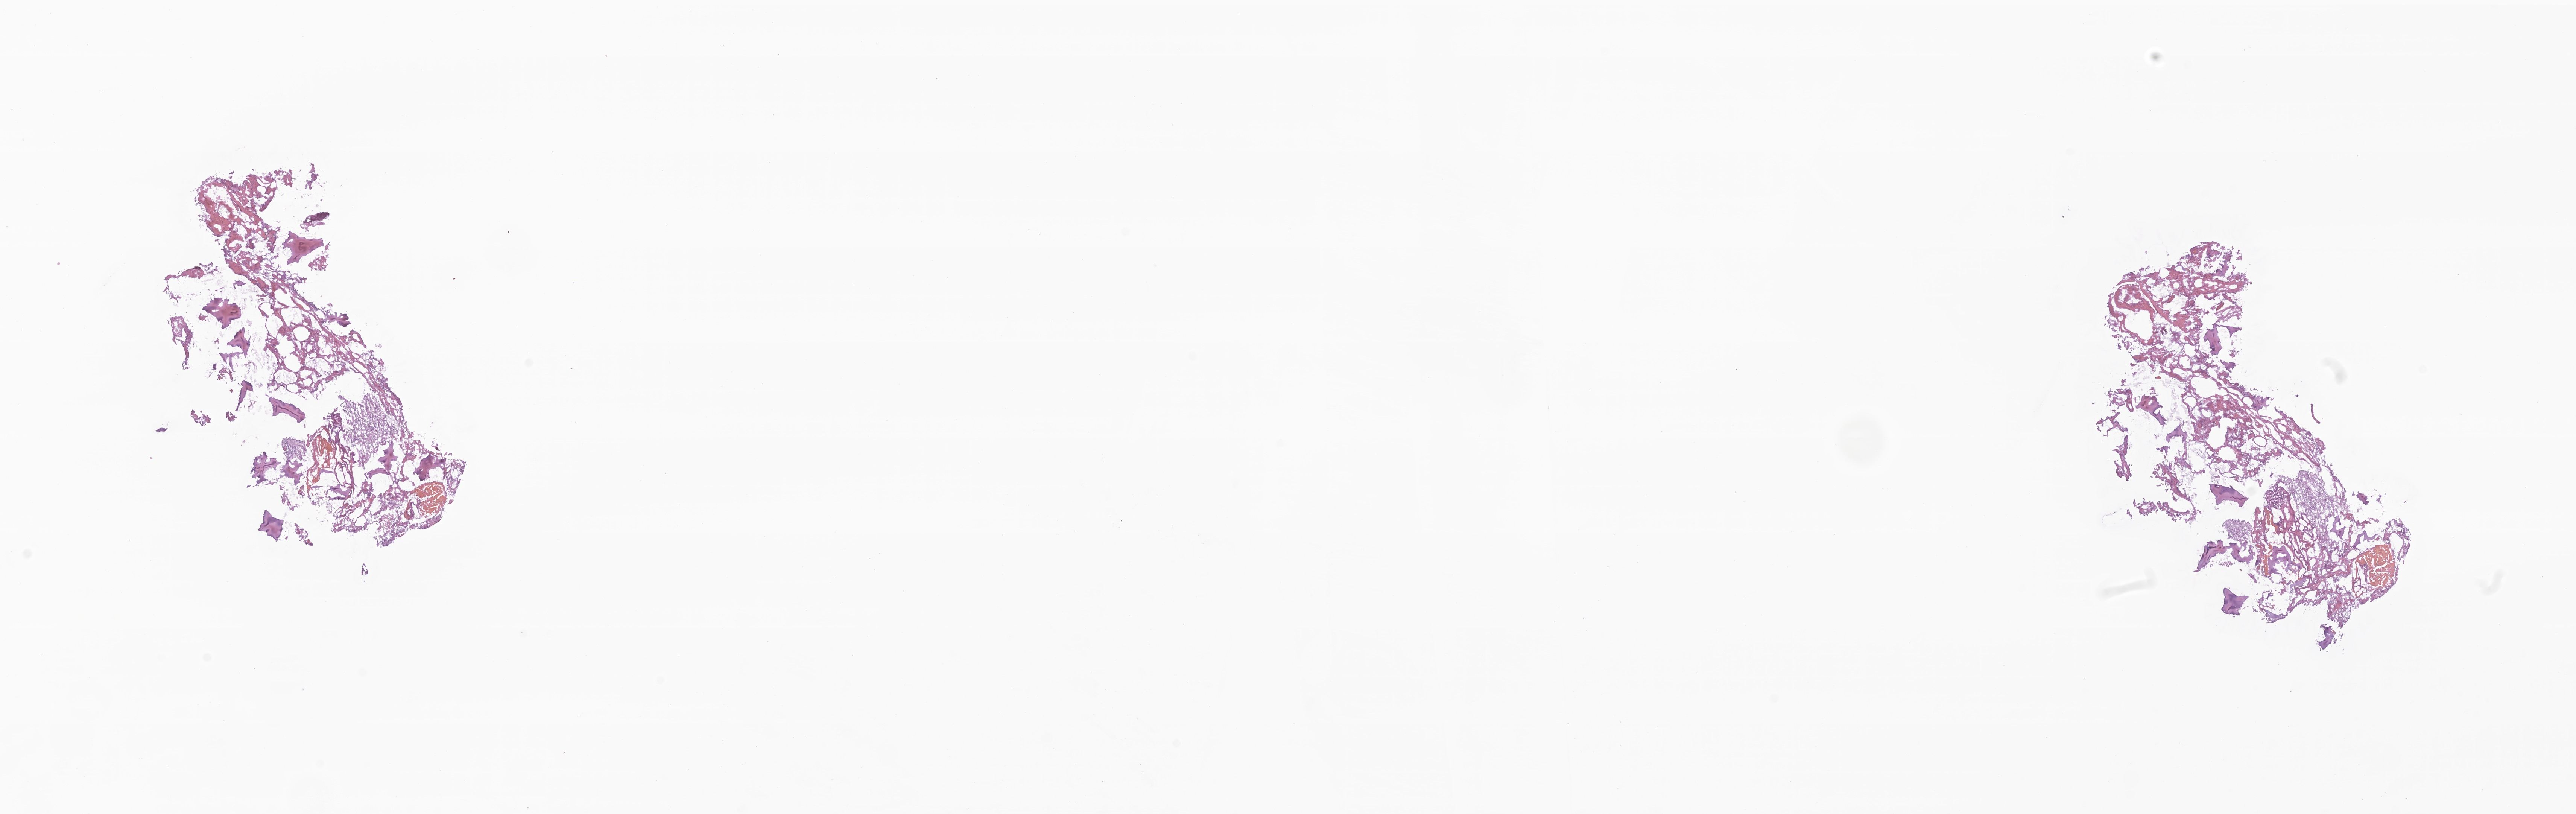
Digitized H&E-stained section of tumor tissue from the brain — low-resolution overview of the scanned area, about 28.9 x 9.1 mm, frozen section (OCT-embedded). Female patient, age 87 months (7 years 3 months).
Diagnosis (ICD-O-3 morphology term): Ependymoma, anaplastic.